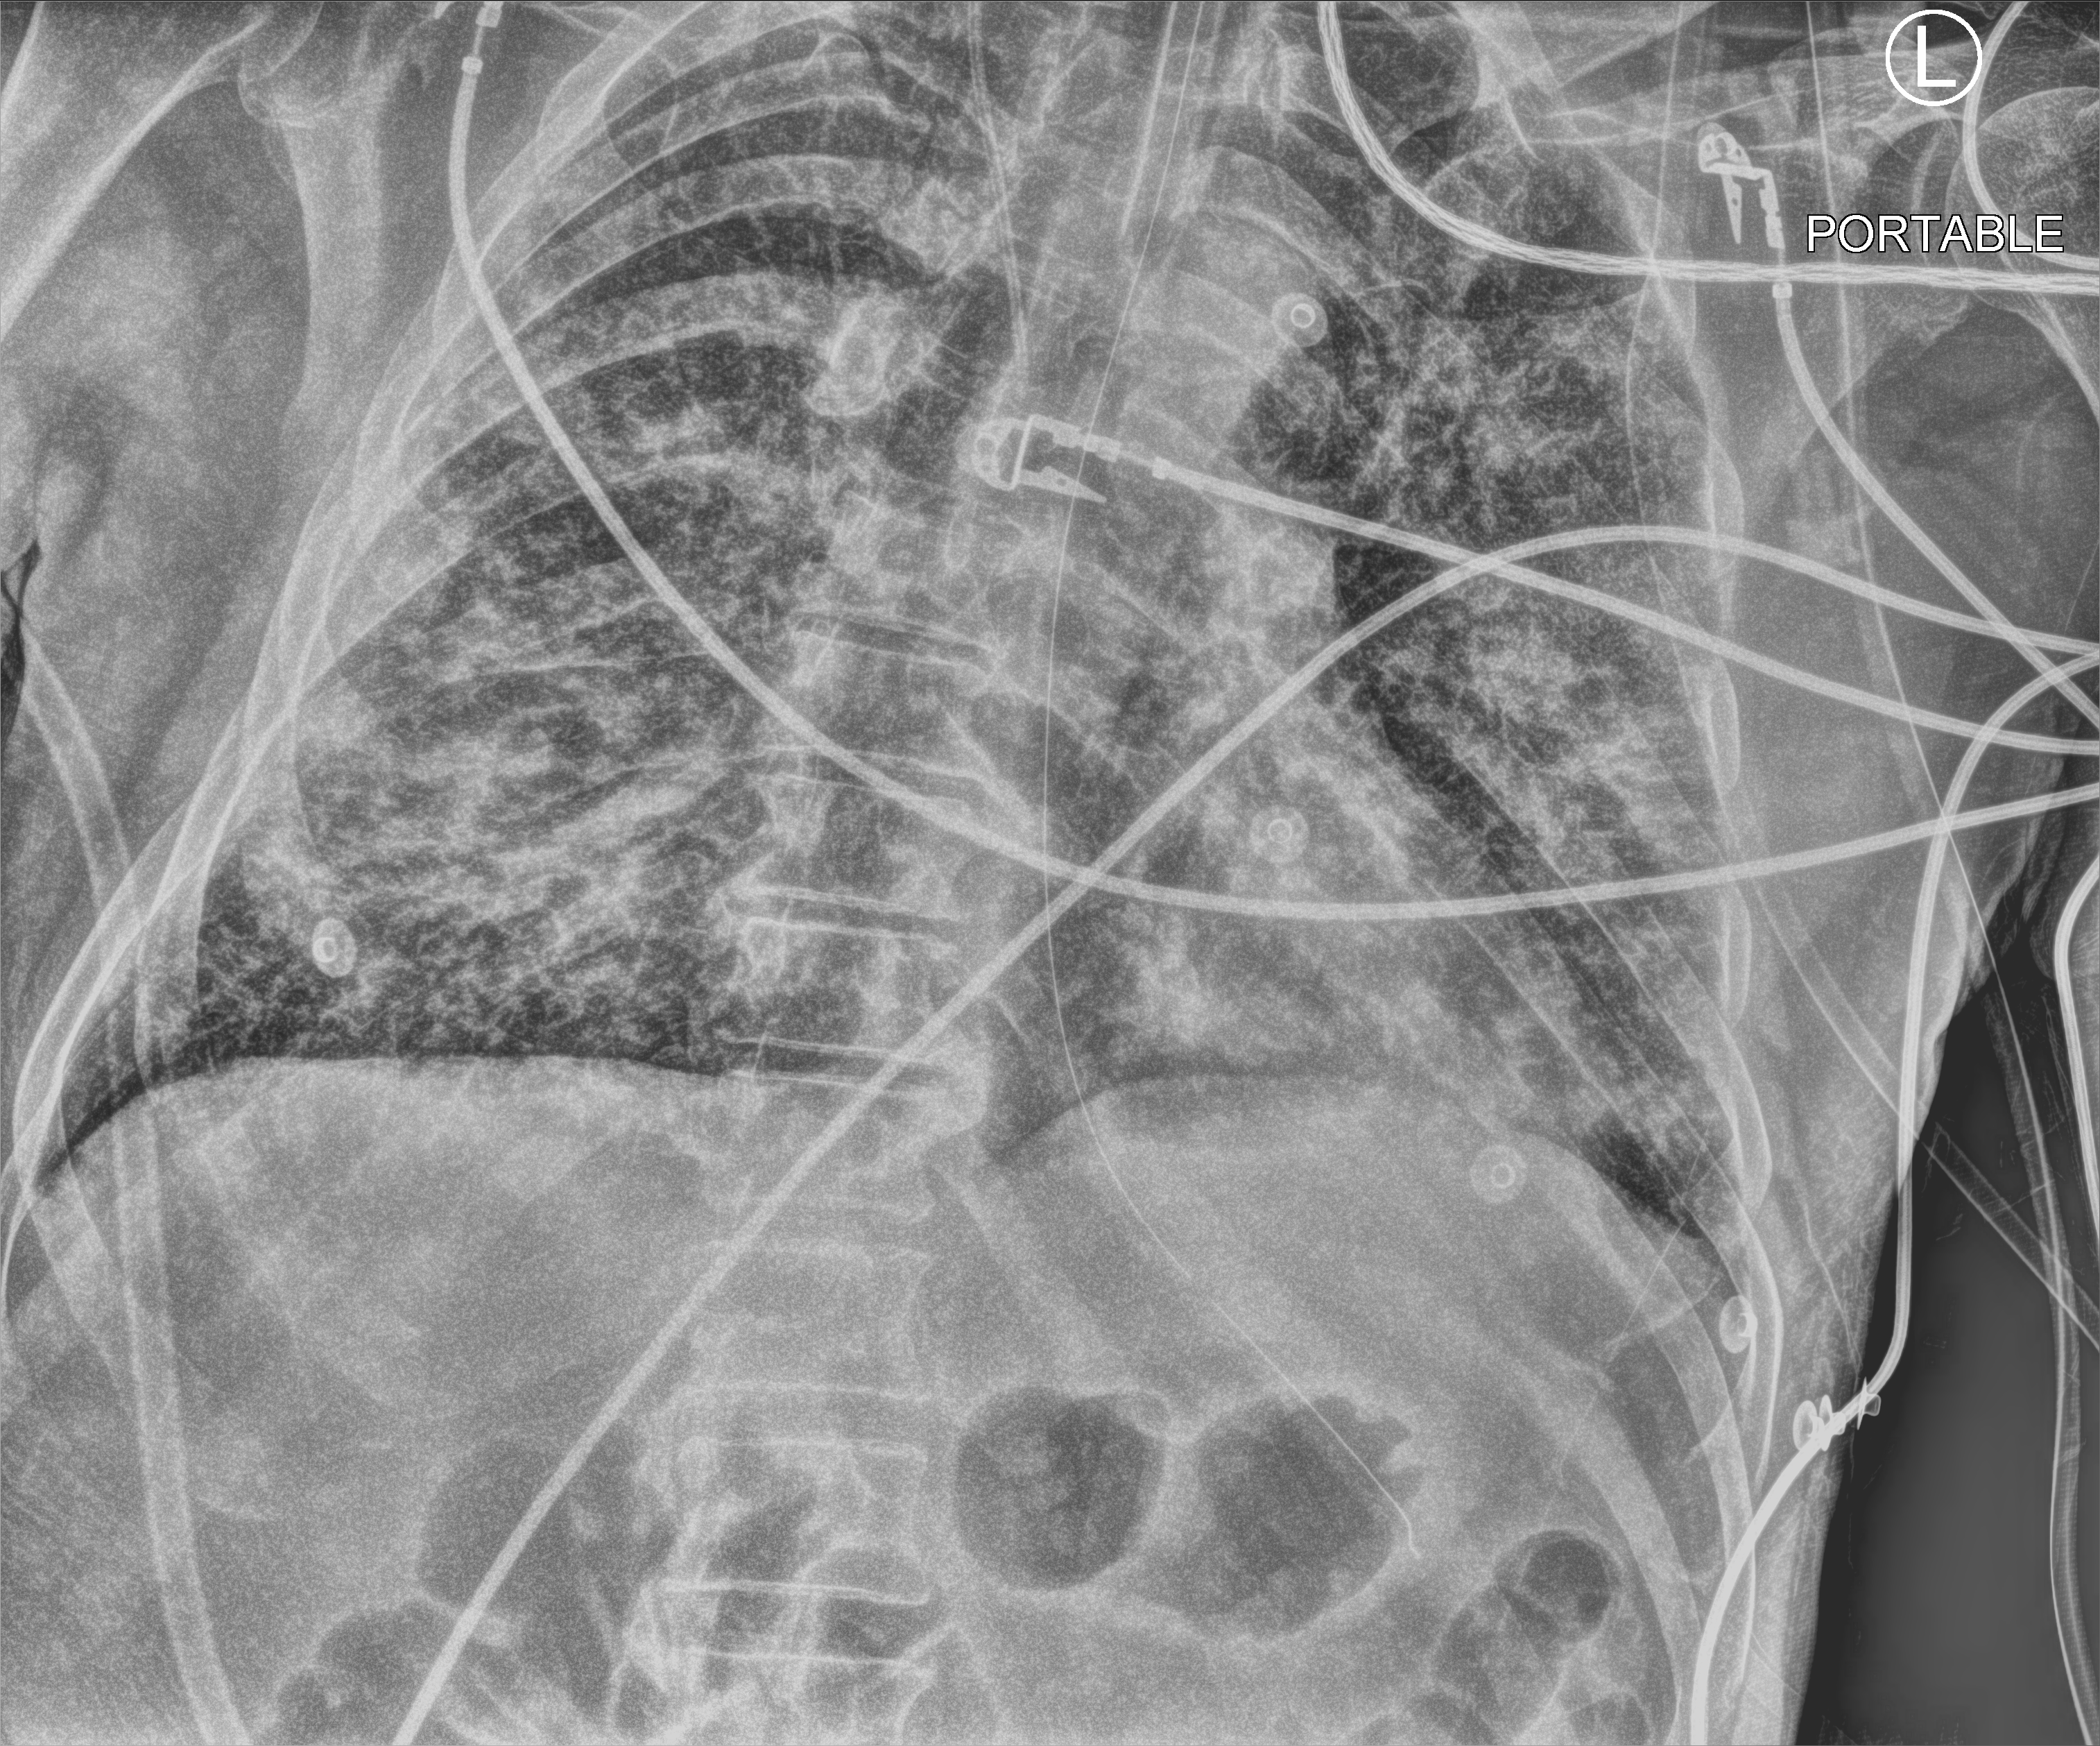
Chest X-ray (portable). Male patient hospitalised with COVID-19, age 60–74 years.
Hospital-stay facts (about this admission, not read from this image; timing relative to this image not recorded):
- admitted to intensive care during this hospital stay: yes